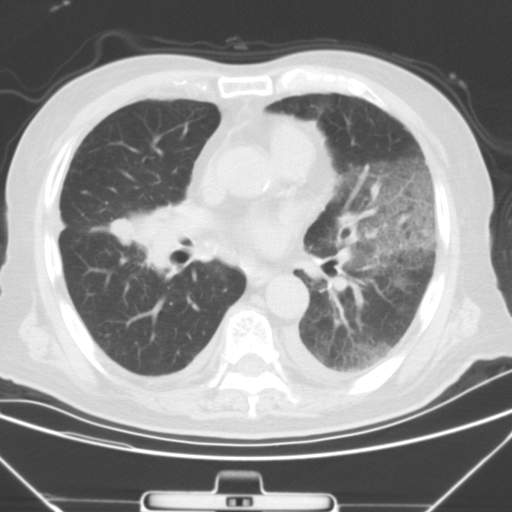
Chest CT, one axial slice; position 17 of 43 along the scan axis; 120 kVp; lung window (W 1500 / L -600 HU); 5 mm slice thickness; 512 × 512 image matrix, field of view 343 × 343 mm. Patient: male, 85 years. Case-level facts recorded for this patient, not image findings: clinical TNM (as recorded): T4 N3 M2.
Structures marked on this image (bounding box drawn by a radiologist):
- lung tumour (recorded histology: squamous cell carcinoma): bounding box [x1, y1, x2, y2] px = [105, 199, 210, 283]